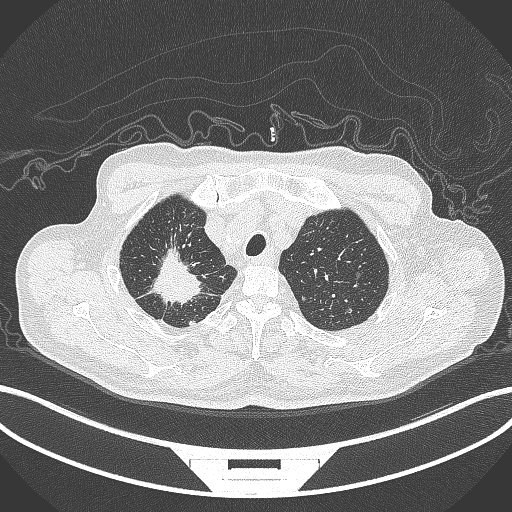
Chest CT, one axial slice. Position 327 of 407 along the scan axis. Reconstruction kernel B70f. Lung window (W 1500 / L -600 HU). 1 mm slice thickness. 512 × 512 image matrix, field of view 400 × 400 mm. Patient: male, 69 years. Case-level facts recorded for this patient, not image findings: clinical TNM (as recorded): T1c N1 M1.
Annotated regions visible in this slice (rectangle marked by the reading radiologist):
- lung tumour (recorded histology: adenocarcinoma): bounding box (x1, y1, x2, y2) in pixels: (147, 241, 206, 307)